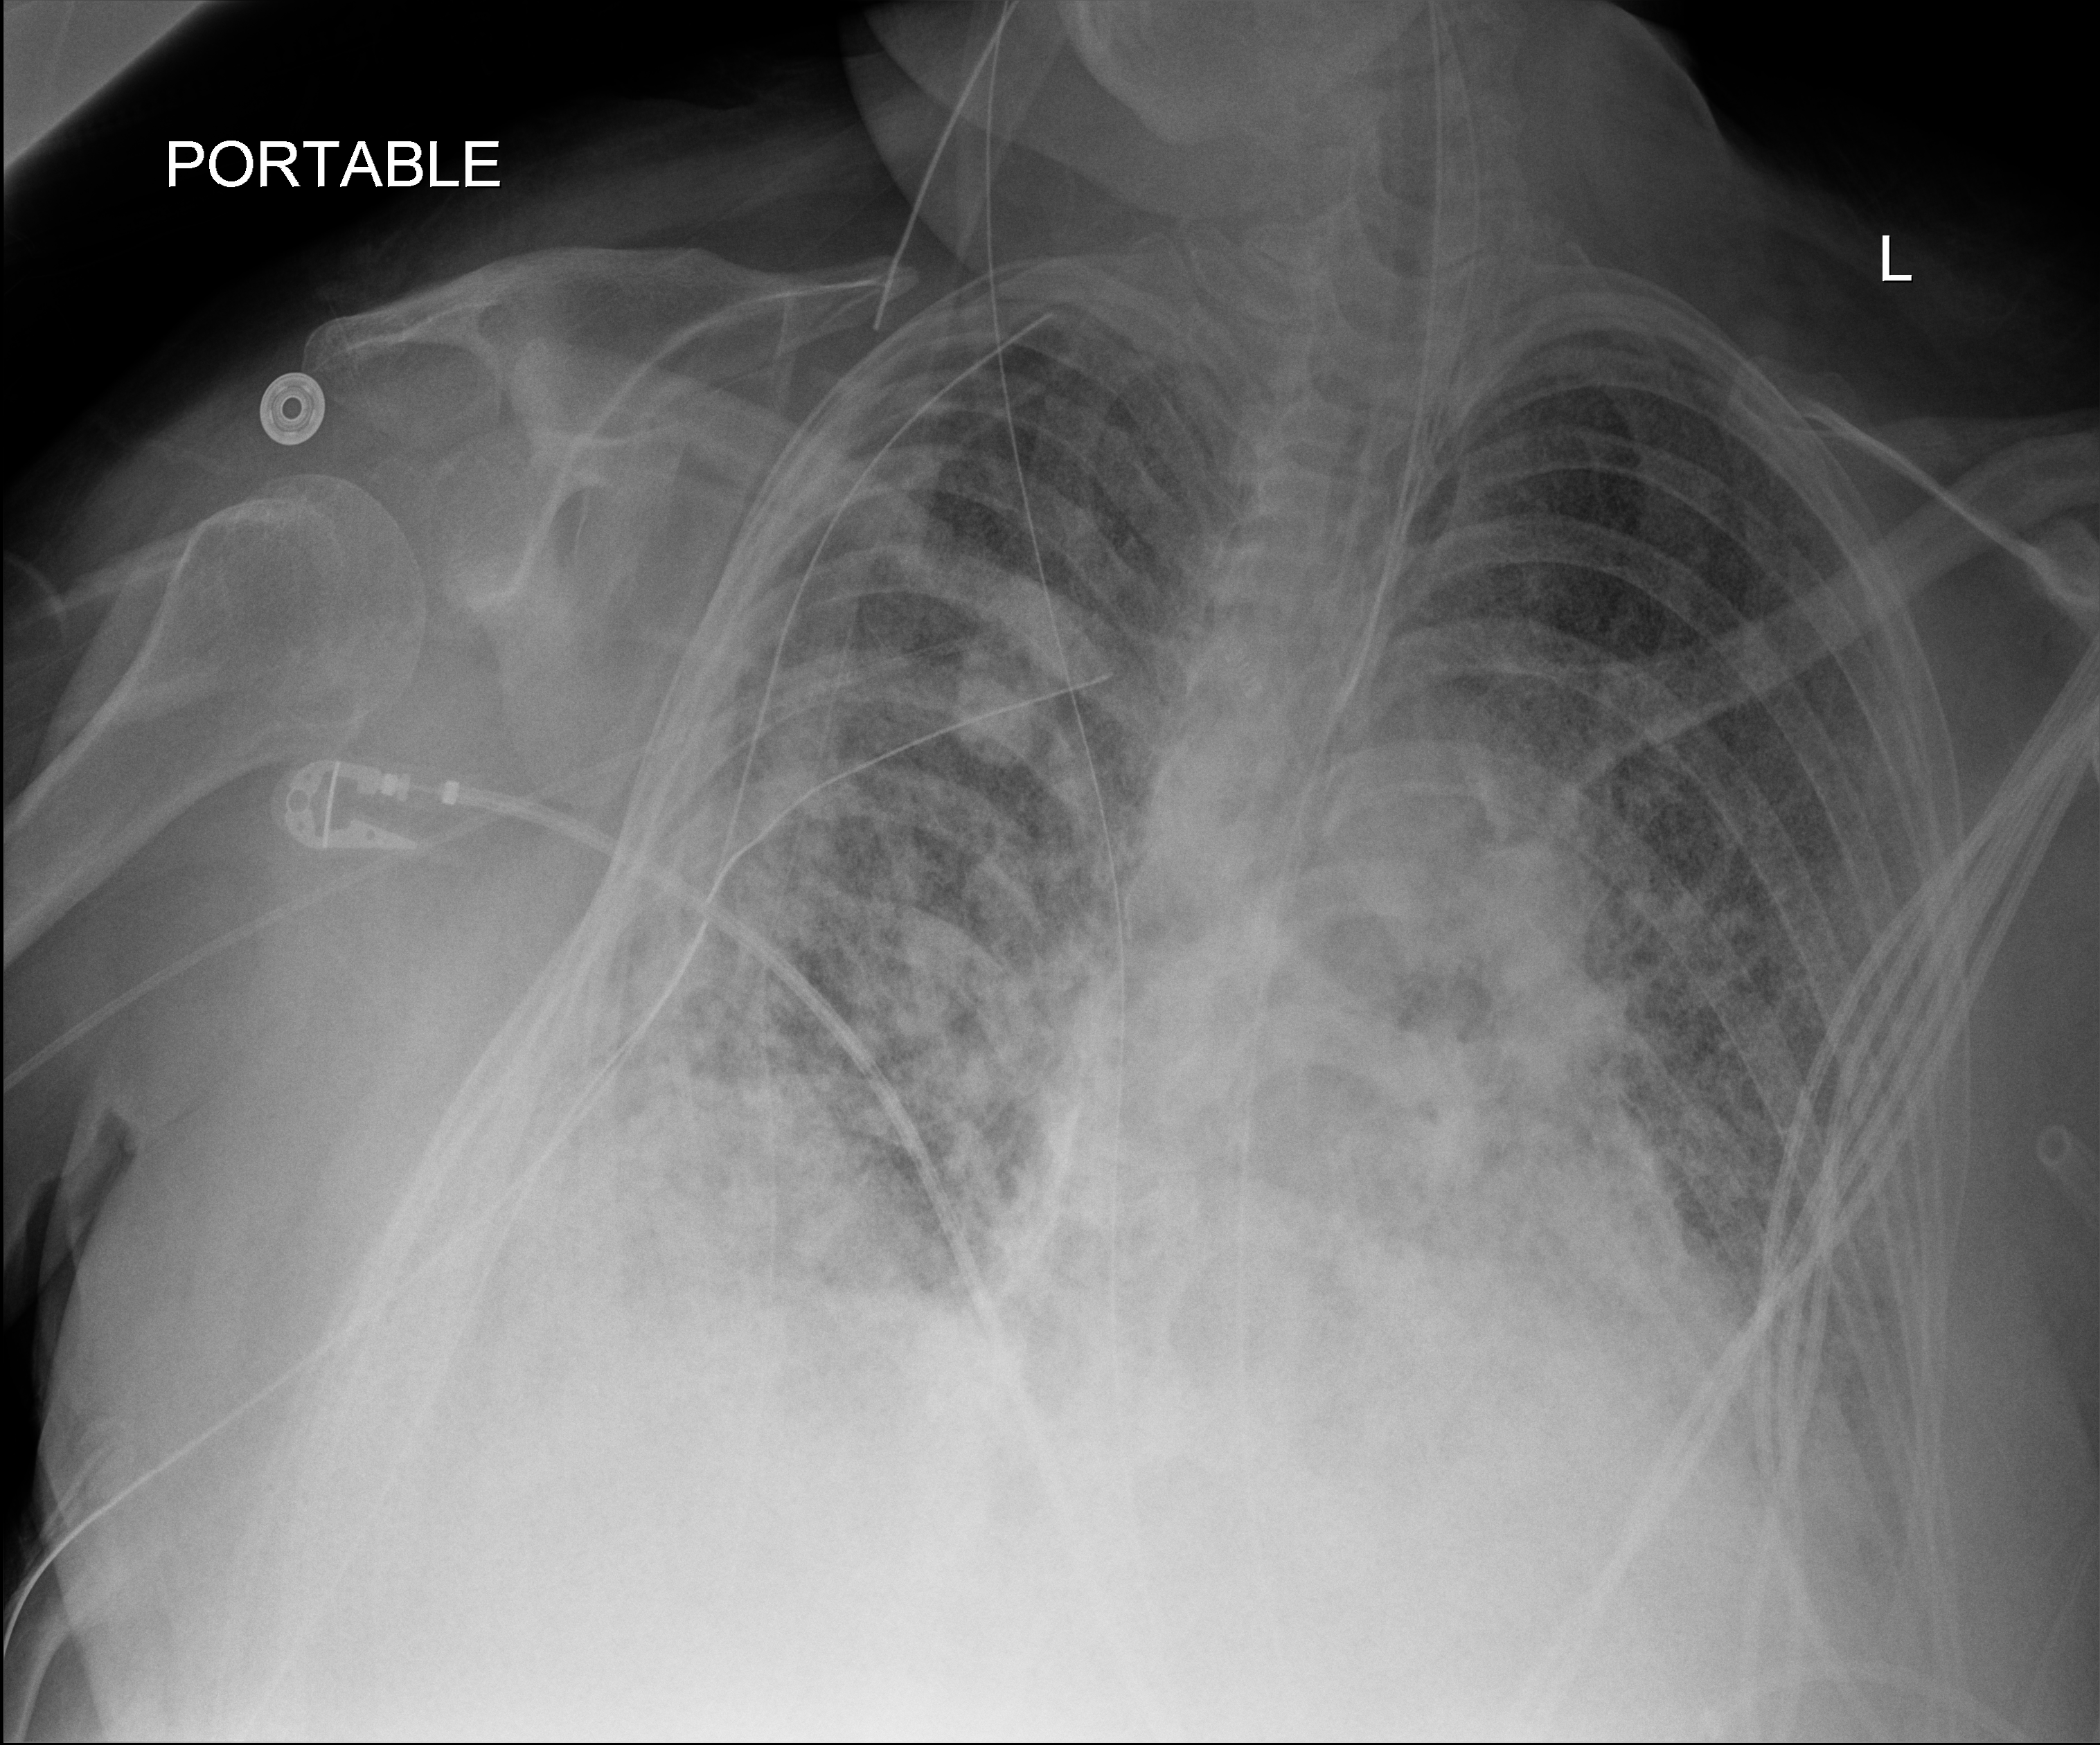
Bedside chest radiograph (digital radiography), anteroposterior (AP) projection. Patient hospitalised with COVID-19, aged 18–59 years.
Admission-level facts for this patient (not findings on this image; timing relative to this image not recorded):
- admitted to intensive care during this hospital stay: yes